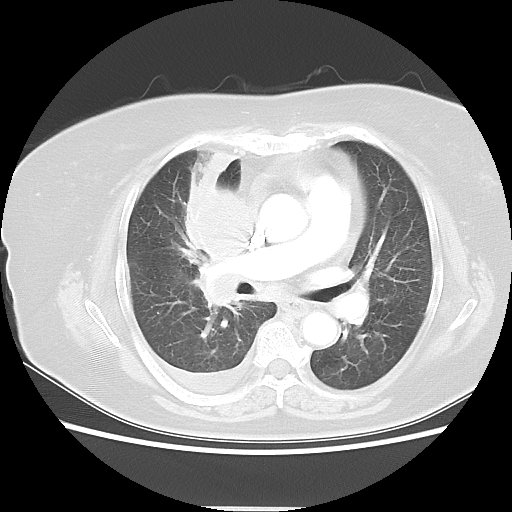
Chest CT, one axial slice; position 27 of 48 along the scan axis; reconstruction kernel LUNG; 120 kVp; lung window (W 1500 / L -600 HU); 512 × 512 image matrix. Patient: female, 73 years. From the clinical record (not read from this slice): clinical TNM (as recorded): T3 N3 M1b.
Outlined on this slice (rectangle marked by the reading radiologist):
- lung tumour (recorded histology: small cell carcinoma): bounding box (x1, y1, x2, y2) in pixels: (181, 150, 266, 321)